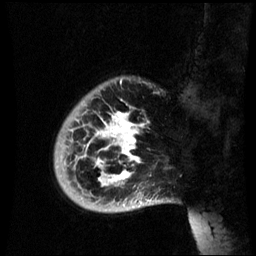
Breast MRI (dynamic contrast-enhanced), one sagittal slice; slice 10 of 60 in the series (ordered by position); dynamic contrast-enhanced series, image 2 of 3 at this slice position (ordered by acquisition); 1.5 T; TE 4.2 ms, TR 8.9 ms; 2.6 mm slice thickness; 256 × 256 image matrix, field of view 220 × 220 mm. Patient: female, 35 years. Case-level facts recorded for this patient, not image findings: setting: breast cancer imaged before/during neoadjuvant chemotherapy; receptor status: HR-positive, HER2-negative.
Structures marked on this image (semi-automatic segmentation, software-assisted and operator-edited):
- analysis volume of interest (the breast-tissue region the enhancement analysis was run in; not a lesion): bounding box [x1, y1, x2, y2] px = [54, 76, 164, 213]
- tumour enhancement mask (voxels above the 70 % enhancement threshold inside the analysis volume of interest): [83, 112, 139, 185]